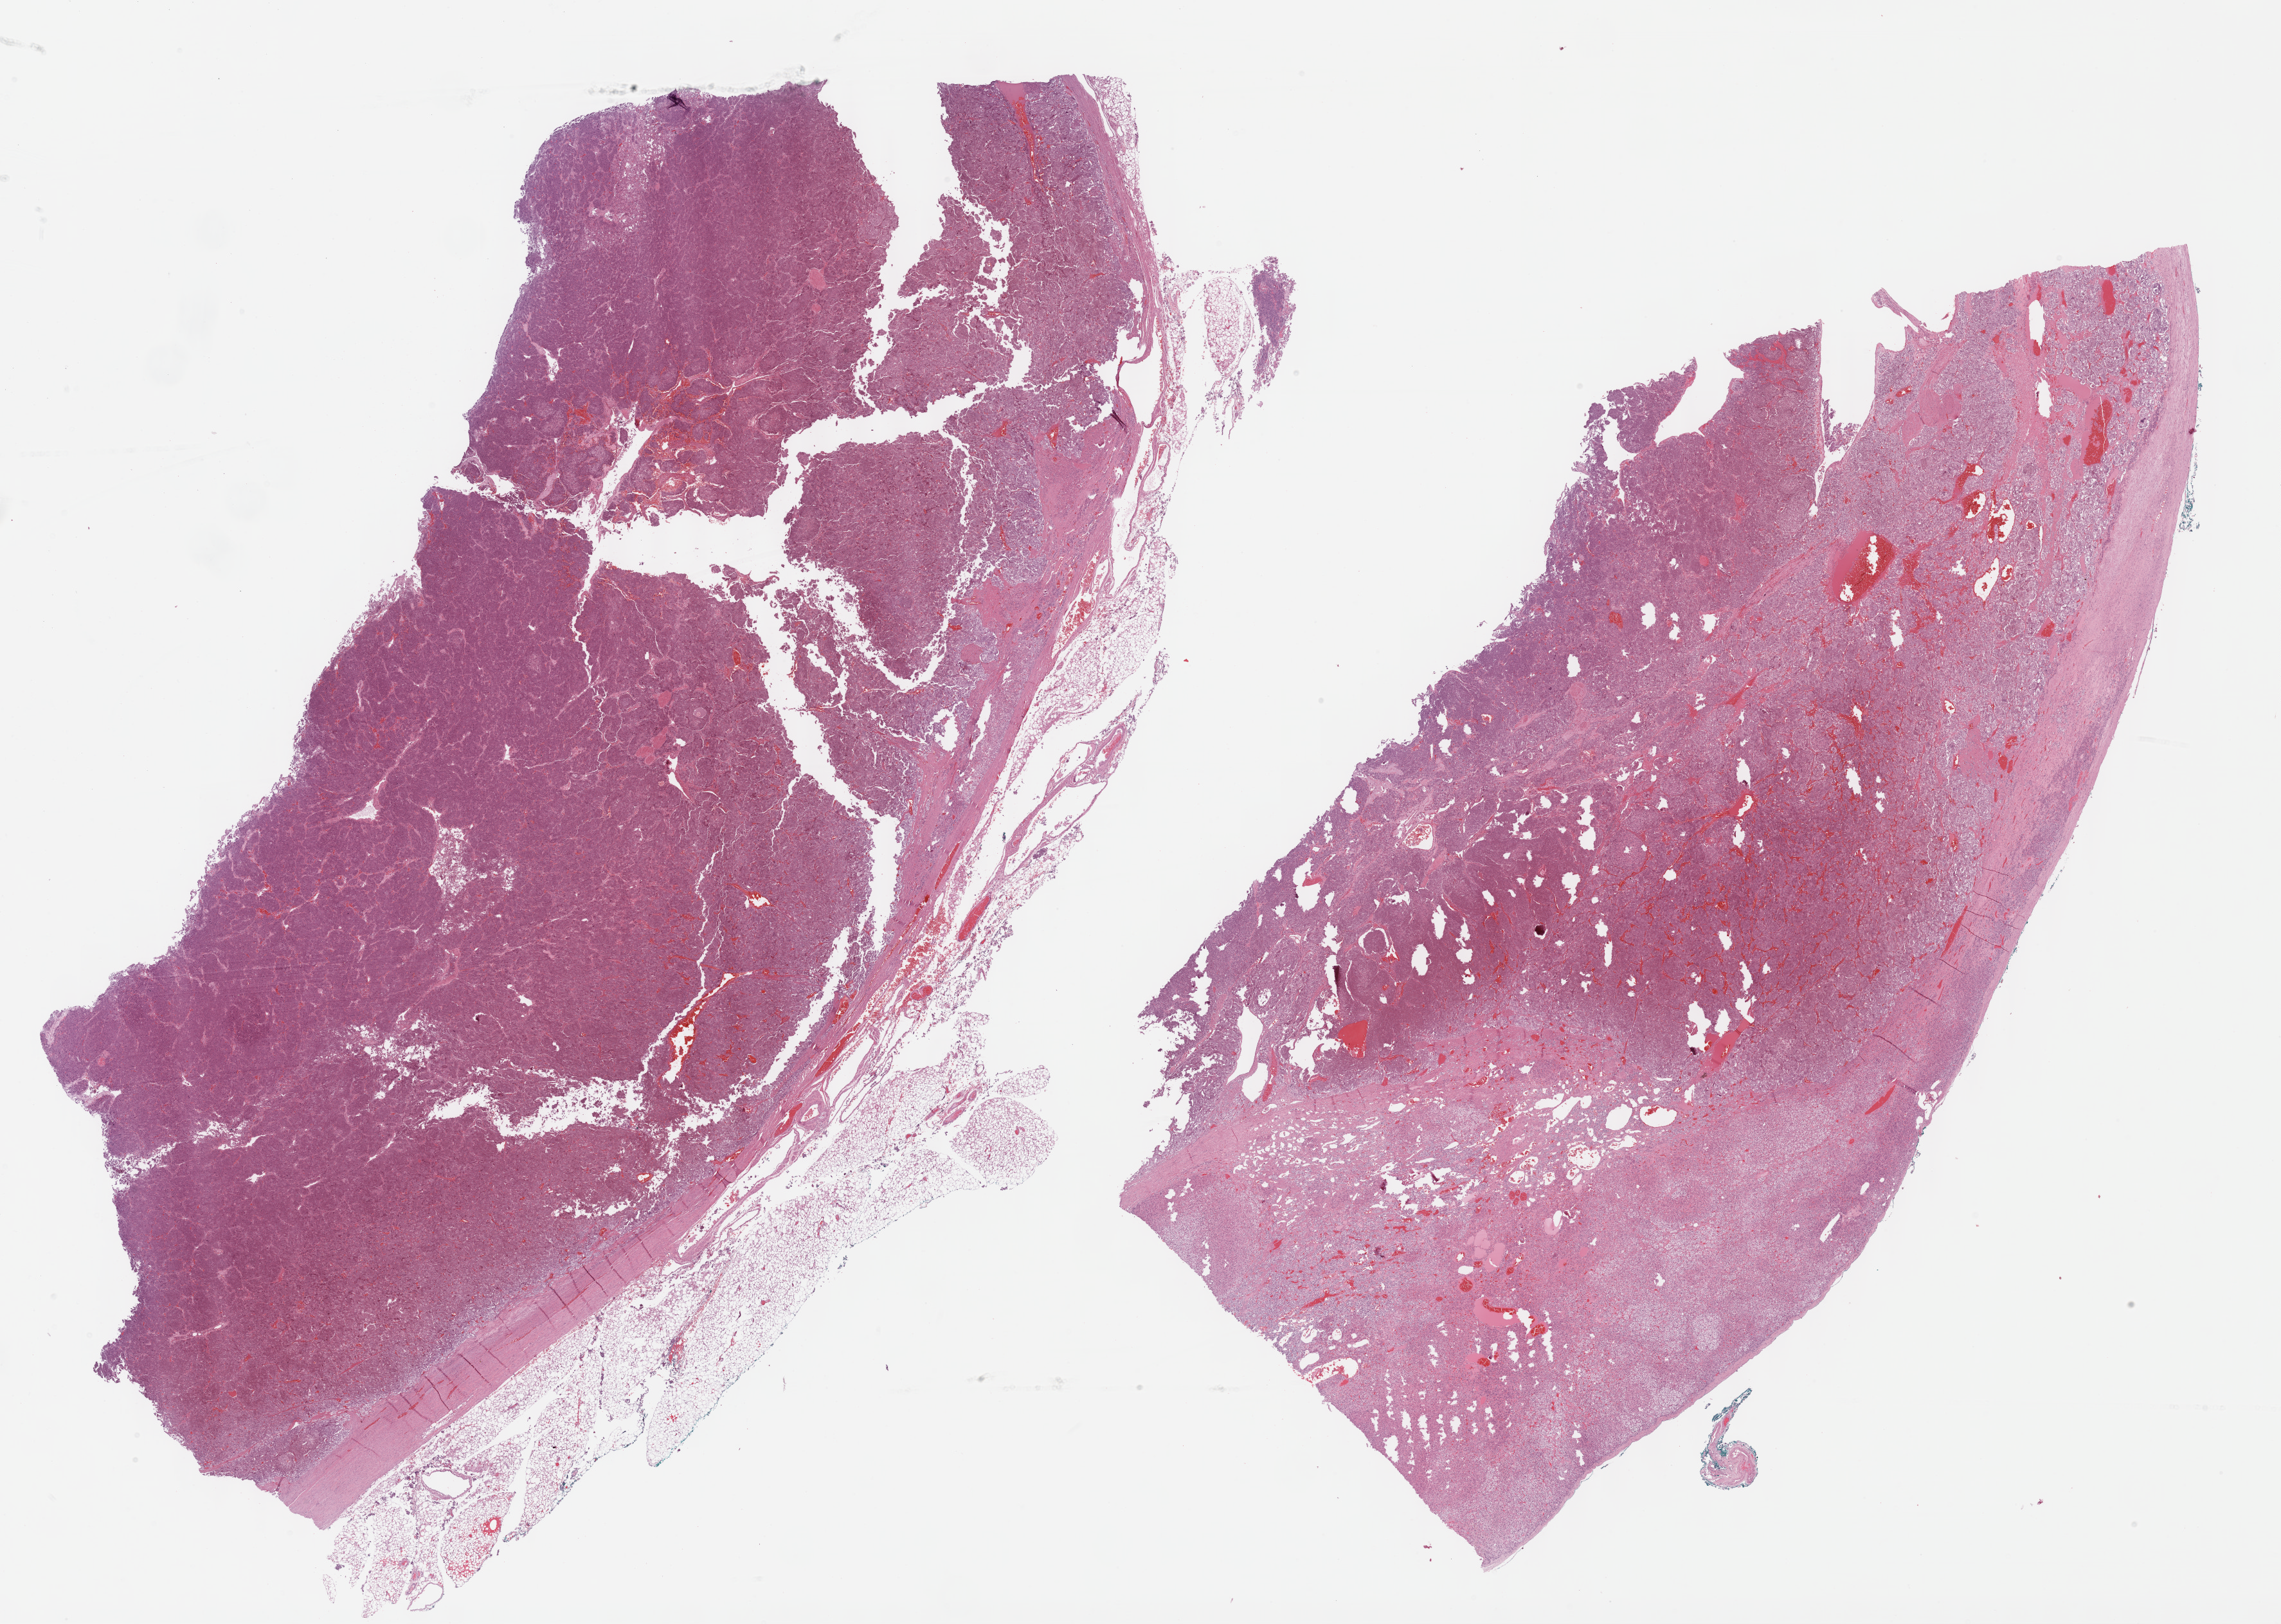
Digitized H&E-stained tissue section (whole slide) — low-resolution overview of the scanned area, about 28.7 x 20.4 mm (slide scanned at 40x); formalin-fixed paraffin-embedded (FFPE) diagnostic section; primary tumour sample from the adrenal gland. Male, age 62 years at initial diagnosis.
Lymph nodes positive (case pathology): 2 of 2 examined. Laterality: left. Diagnosis: Pheochromocytoma, malignant.